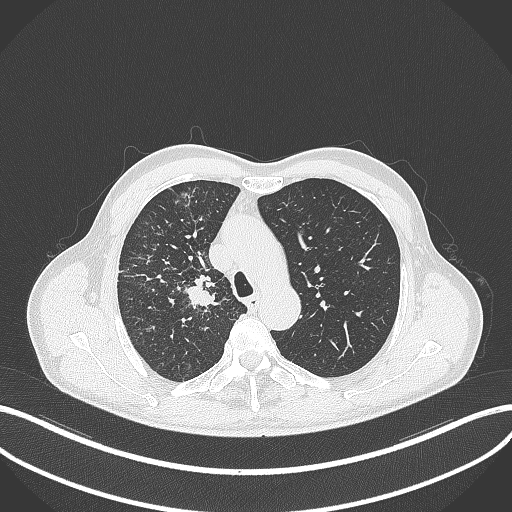
Chest CT, one axial slice. Slice 355 of 490 in the series (ordered by position). Reconstruction kernel B70f. 120 kVp. Lung window (W 1500 / L -600 HU). 1 mm slice thickness. 512 × 512 image matrix, field of view 400 × 400 mm. Patient: male, 69 years. From the clinical record (not read from this slice): clinical TNM (as recorded): T2a N0 M0.
Structures marked on this image (rectangle marked by the reading radiologist):
- lung tumour (recorded histology: adenocarcinoma): bounding box [x1, y1, x2, y2] px = [186, 271, 224, 309]